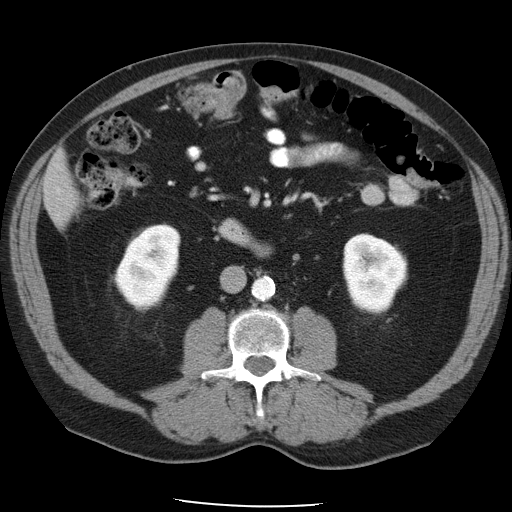
Contrast-enhanced abdominal CT, one axial slice; position 14 of 49 along the scan axis; 120 kVp; intravenous contrast given; soft-tissue window (W 400 / L 40 HU); 5 mm slice thickness; 512 × 512 image matrix, field of view 395 × 395 mm. Male patient, age 68 years. From the clinical record (not read from this slice): diagnosis: colorectal cancer liver metastases, imaged before liver resection.
Annotated regions visible in this slice (outlined manually by an expert reader):
- liver: bounding box [x1, y1, x2, y2] px = [45, 156, 76, 221]